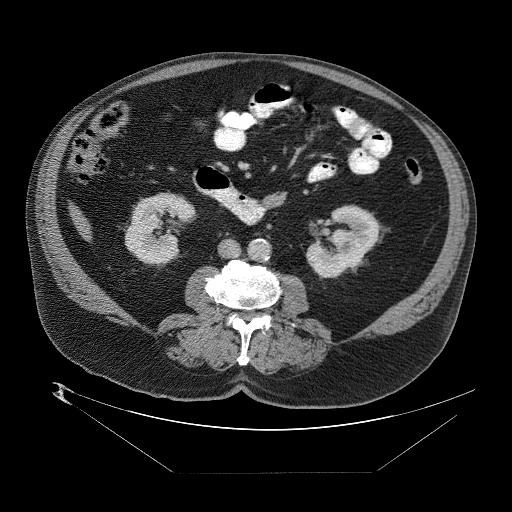
Contrast-enhanced abdominal CT (liver protocol), one axial slice. Slice 3 of 89 in the series (ordered by position). Reconstruction kernel STANDARD. 140 kVp. One of 2 acquisitions stored at this slice position. Soft-tissue window (W 400 / L 40 HU). 512 × 512 image matrix, field of view 480 × 480 mm. Case-level facts recorded for this patient, not image findings: diagnosis: hepatocellular carcinoma (patient treated with transarterial chemoembolisation; whether this scan precedes or follows treatment is not stated here); TNM stage (as recorded): Stage-II; Child-Pugh class: B; tumour differentiation: moderately differentiated; tumour size: 4 cm.
Structures marked on this image (semi-automatically segmented with operator editing):
- abdominal aorta: bounding box [x1, y1, x2, y2] px = [248, 239, 271, 263]
- liver parenchyma outside the tumour (the mass and vessels are separate outlines, so this box may not span the whole liver): [69, 205, 90, 235]